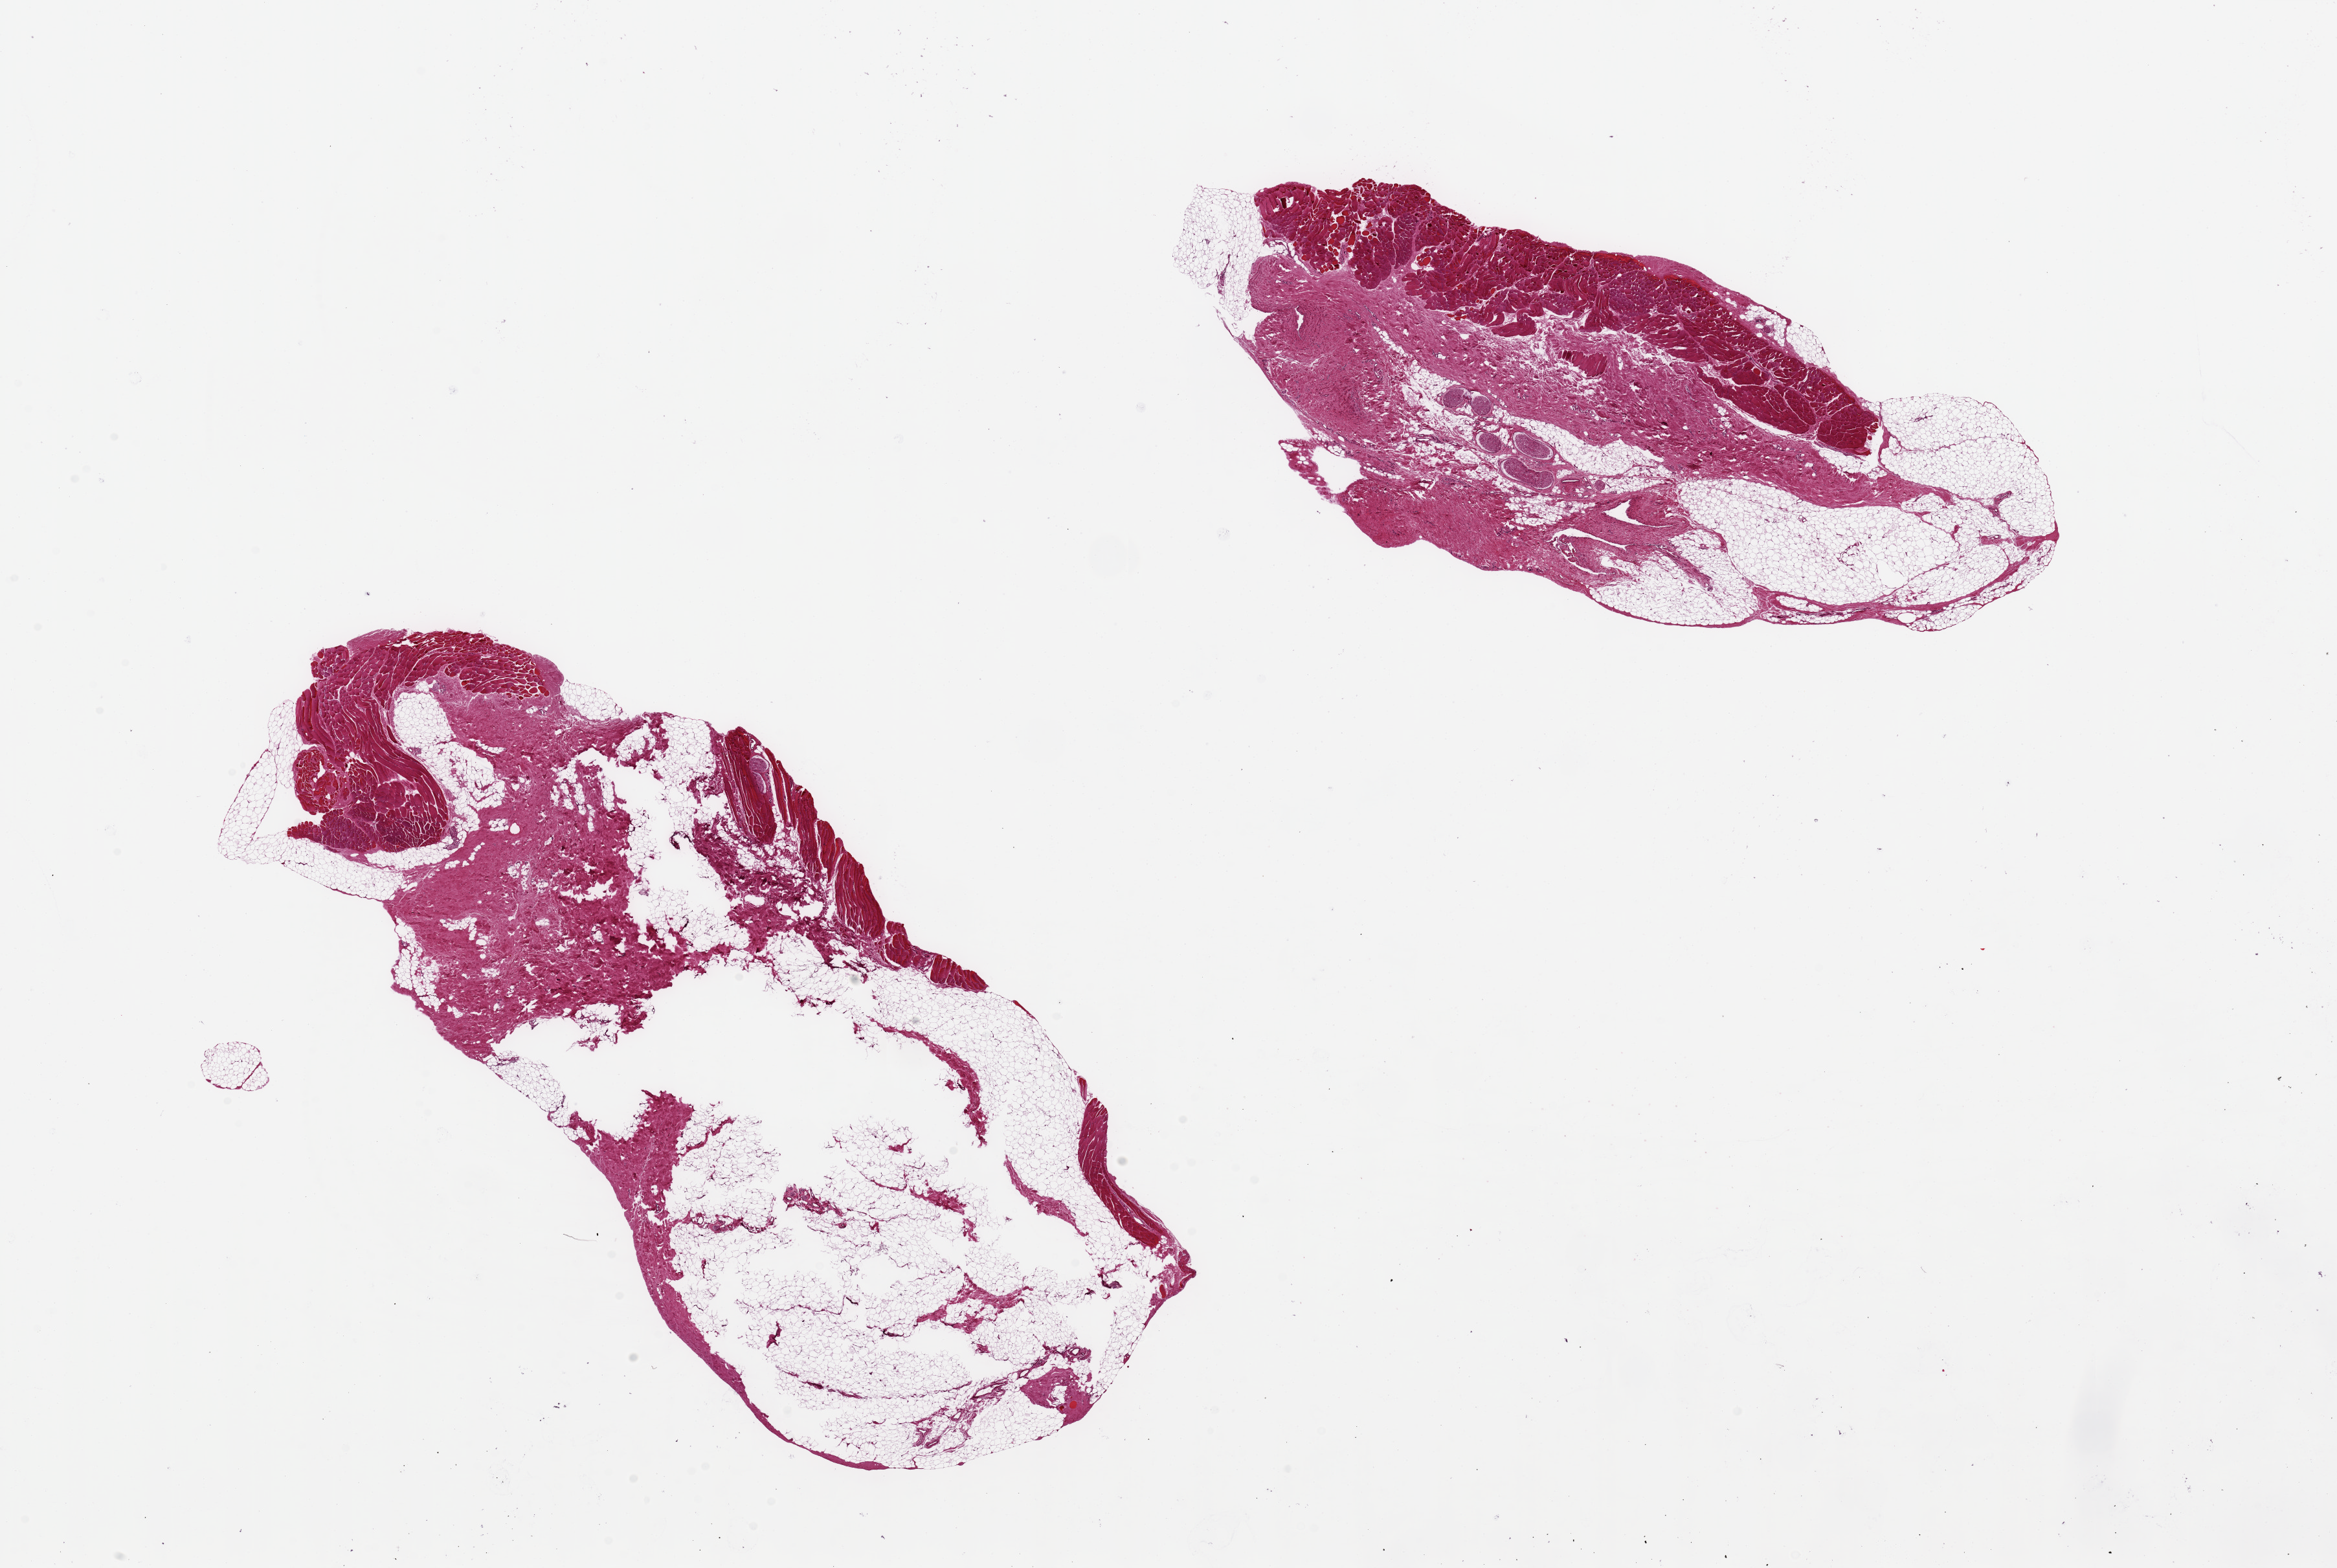
Hematoxylin and eosin (H&E) whole-slide image, whole scanned area (about 28.5 x 19.2 mm, slide scanned at 20x) shown as a low-resolution overview, PAXgene-fixed paraffin-embedded (PFPE) section, section of thyroid (target tissue), donor tissue sample. Donor: female.
* pathologist's review note for this sample: 2 pieces, 11x4&13x6mm; fibroadipose and skeletal muscle NO THYROID